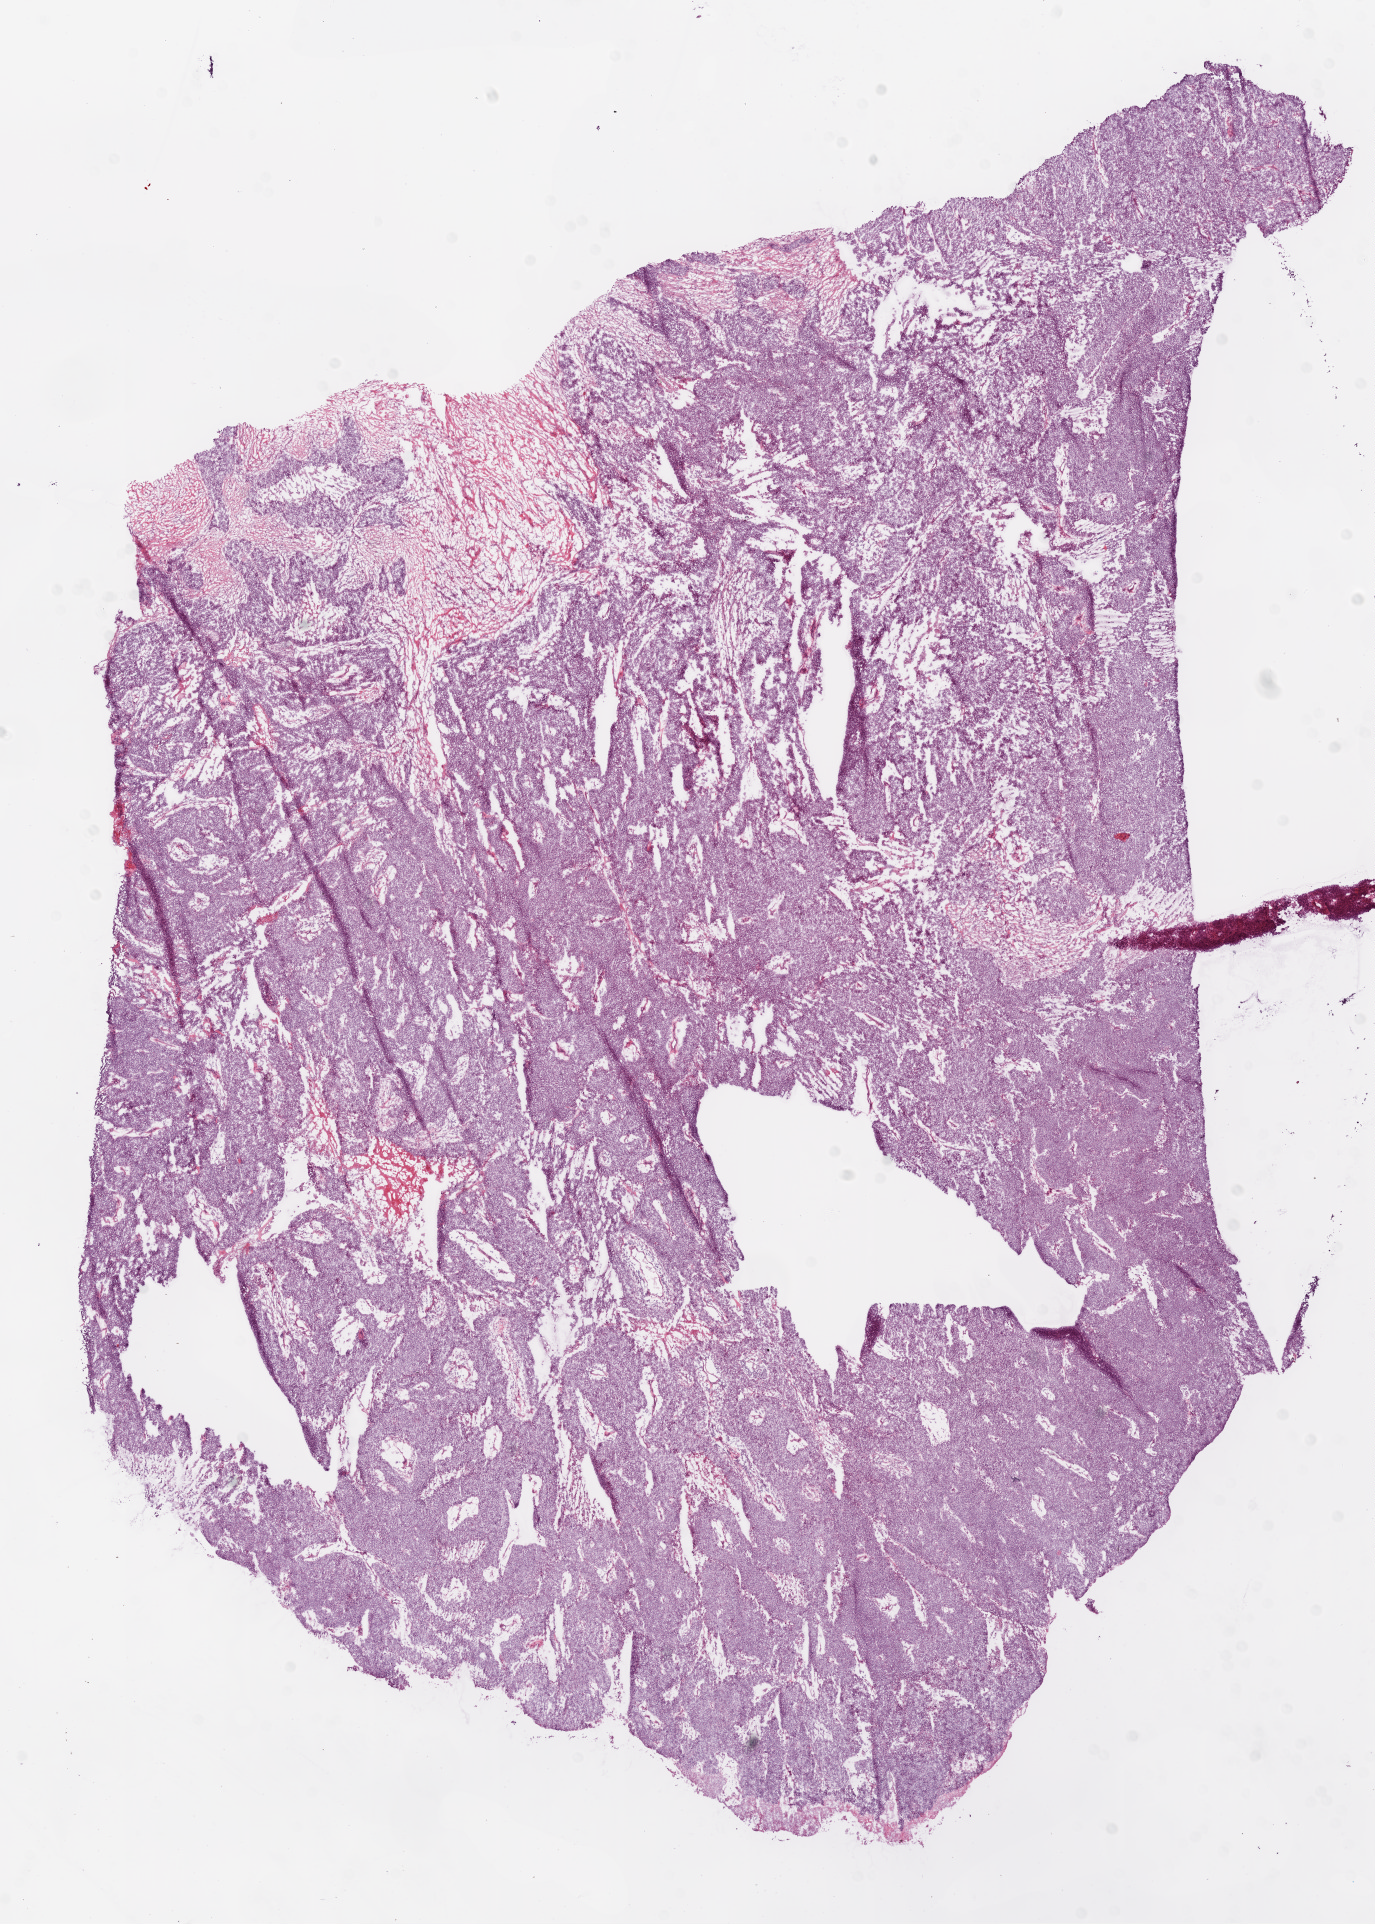
Hematoxylin and eosin (H&E) stained whole-slide image, low-resolution overview of the scanned area, about 11.0 x 15.4 mm (acquisition: 20x scan), frozen section from the bottom of the tissue portion, primary tumour sample from the ovary. Patient: female, age at initial diagnosis 48 years. Histologic grade: G3 (poorly differentiated). Pathologist review of this section (percent, as recorded): tumour cells 89%, tumour nuclei 90%, normal cells 0%, stromal cells 10%, necrosis 1%.
* FIGO stage: IIIB
* diagnosis: Serous cystadenocarcinoma, NOS
* laterality: right